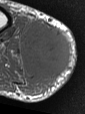
MRI of an extremity soft-tissue mass, one axial slice. Position 19 of 47 along the scan axis. MR volume resampled by the dataset authors to the PET/CT grid (not the native acquisition matrix). 85 × 114 image matrix, field of view 83 × 111 mm. Male patient. From the clinical record (not read from this slice): histological type: pleiomorphic liposarcoma; grade: high; site of the primary tumour: right calf.
Annotated regions visible in this slice (expert contour drawn on MRI and transferred to this co-registered scan by the dataset authors):
- gross tumour volume including surrounding oedema: bounding box (x1, y1, x2, y2) in pixels: (20, 19, 73, 95)
- gross tumour volume (mass): (20, 23, 73, 79)